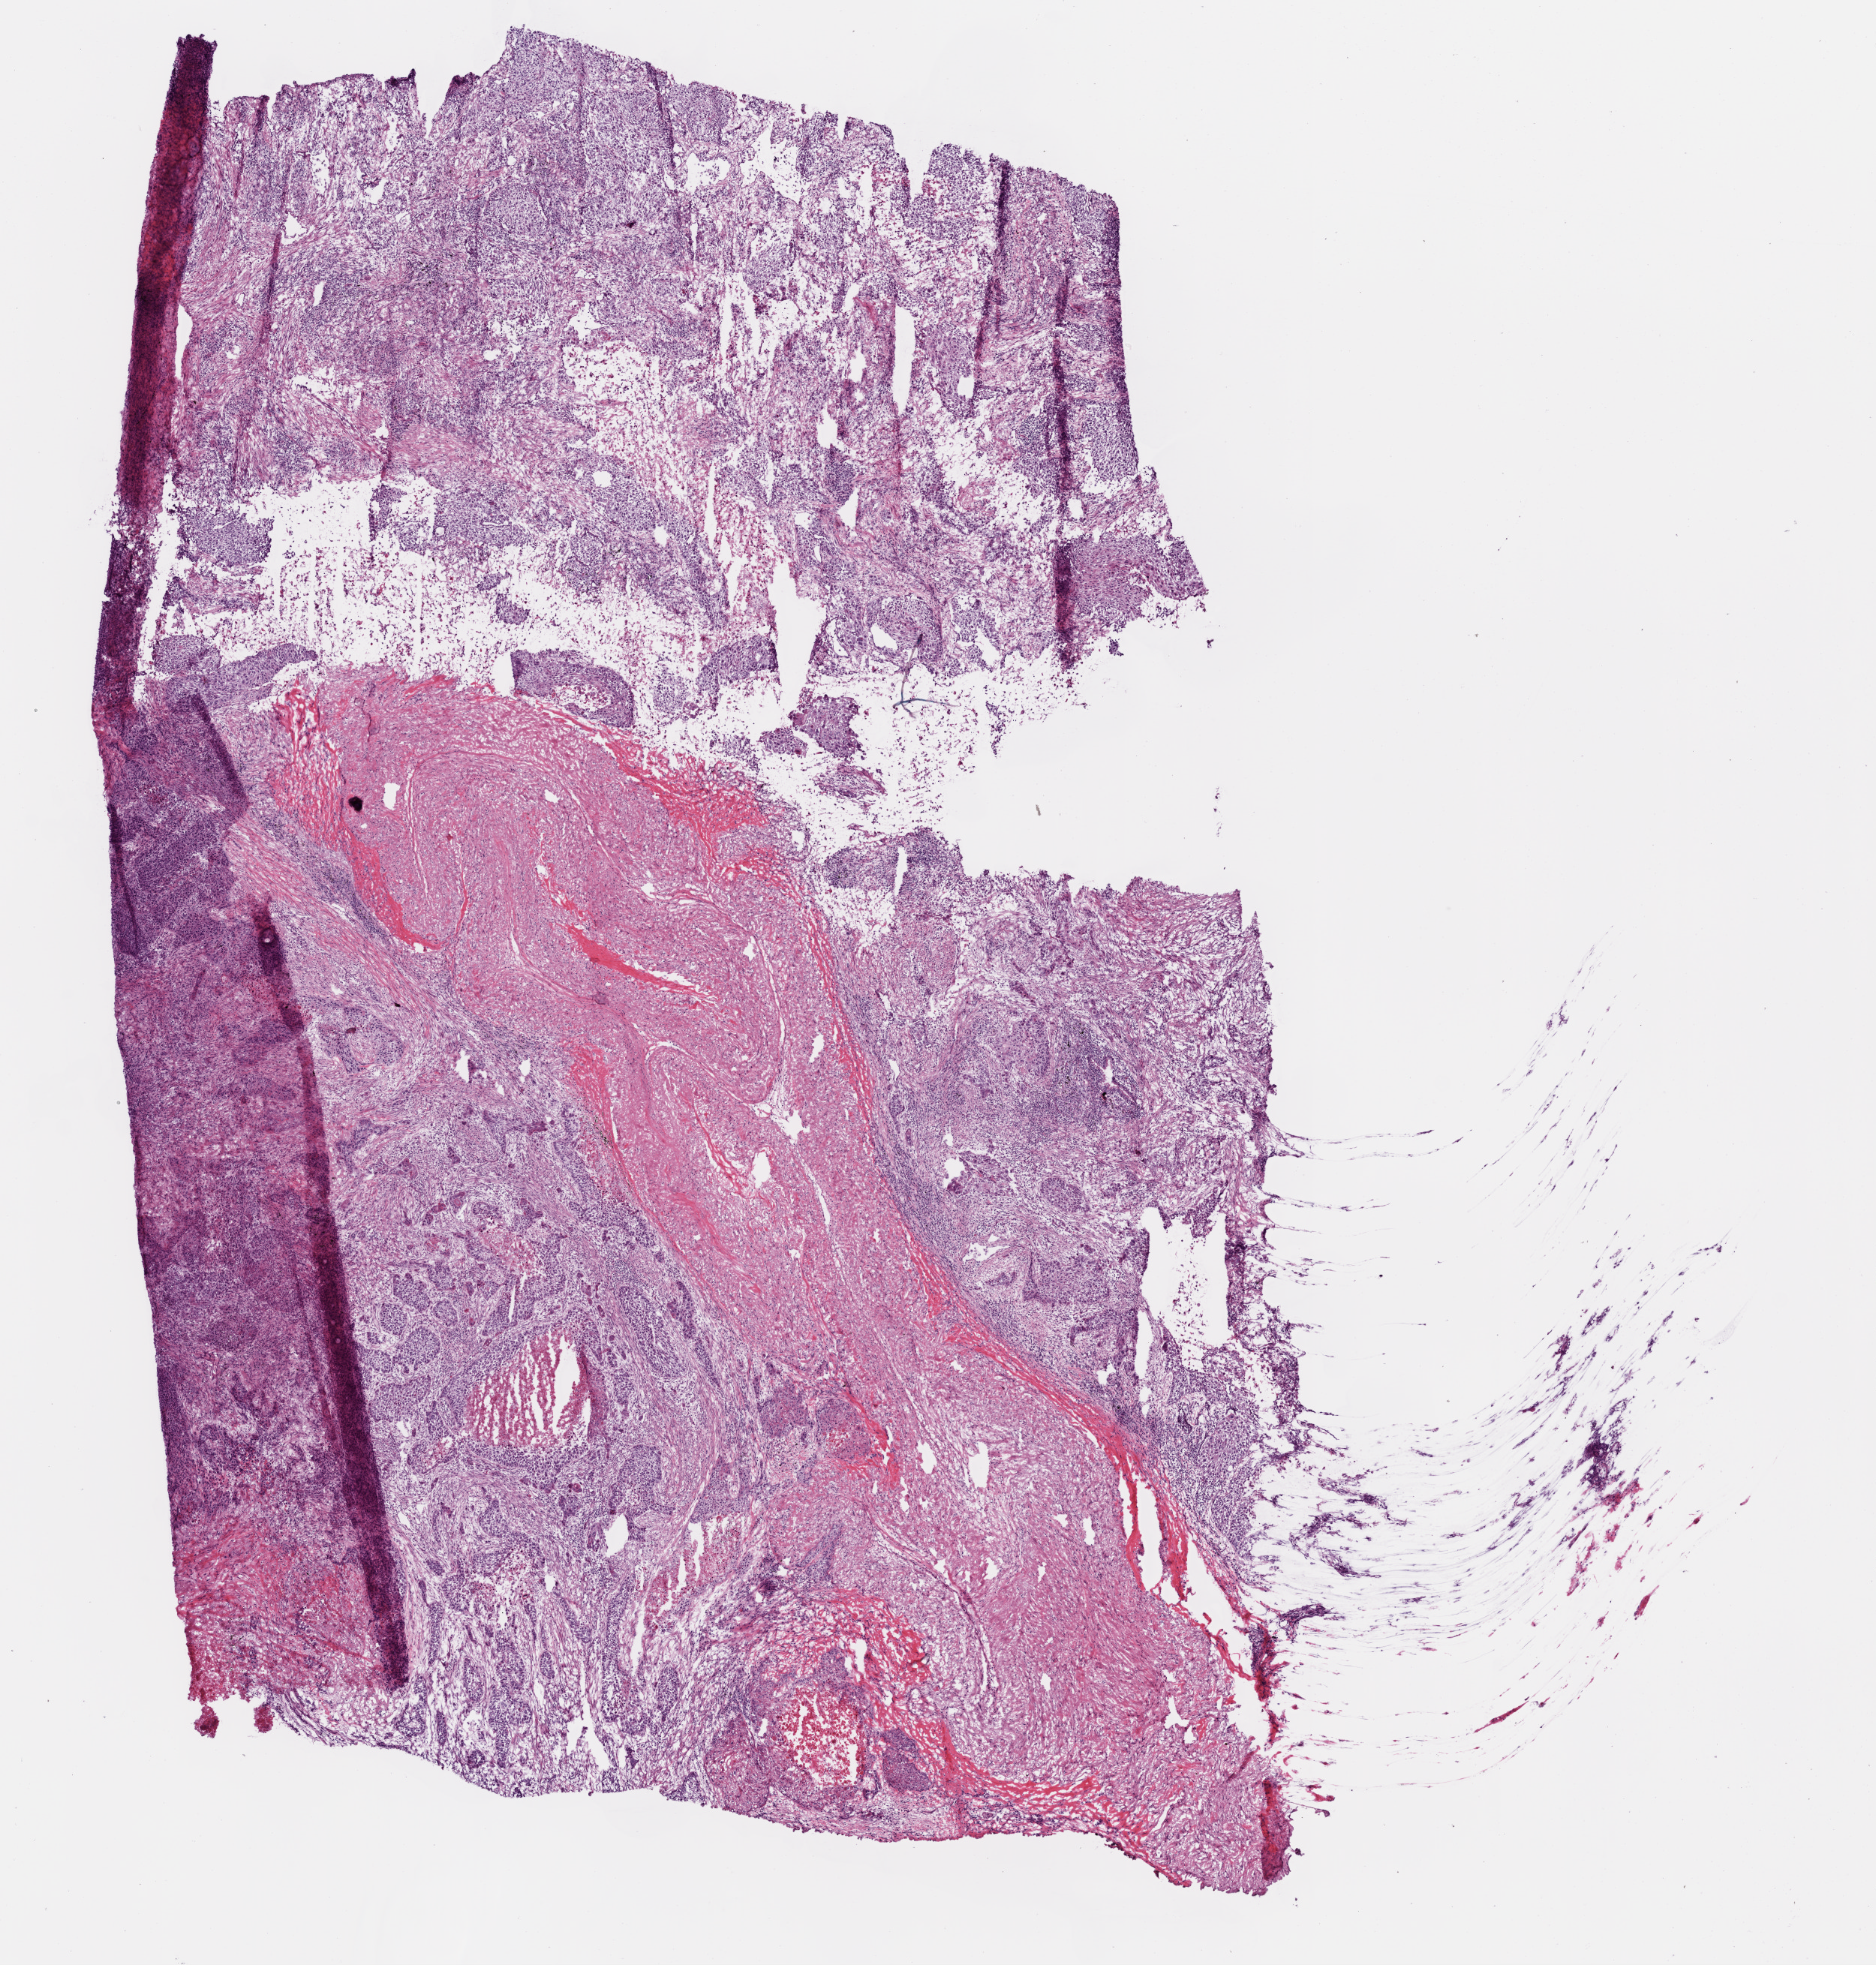
Digitized Hematoxylin and eosin (H&E) stained tissue section (whole slide) — shown as a low-resolution overview of the whole scanned area (about 10.0 x 10.5 mm, acquisition: 20x scan); frozen section from the bottom of the tissue portion; sample: primary tumour, lung. Male, age 72 years at initial diagnosis. Slide review estimates, as recorded: tumour cells 40%, tumour nuclei 60%, normal cells 25%, stromal cells 30%, necrosis 5%. Inflammatory infiltration, as recorded: lymphocyte infiltration 25%.
• laterality: right
• diagnosis: Squamous cell carcinoma, NOS
• AJCC pathologic stage: IIB (5th edition)